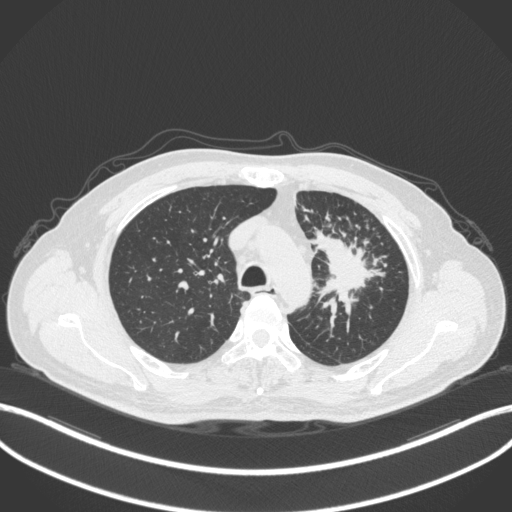
Chest CT, one axial slice. Slice 266 of 386 in the series (ordered by position). Reconstruction kernel B31f. 120 kVp. Lung window (W 1500 / L -600 HU). 1 mm slice thickness. 512 × 512 image matrix, field of view 400 × 400 mm. Male patient, age 69 years. From the clinical record (not read from this slice): clinical TNM (as recorded): T2a N2 M0; histopathological grade: G2-3.
Structures marked on this image (bounding box drawn by a radiologist):
- lung tumour (recorded histology: adenocarcinoma): bounding box <311,229,379,303> (left, top, right, bottom; pixels)